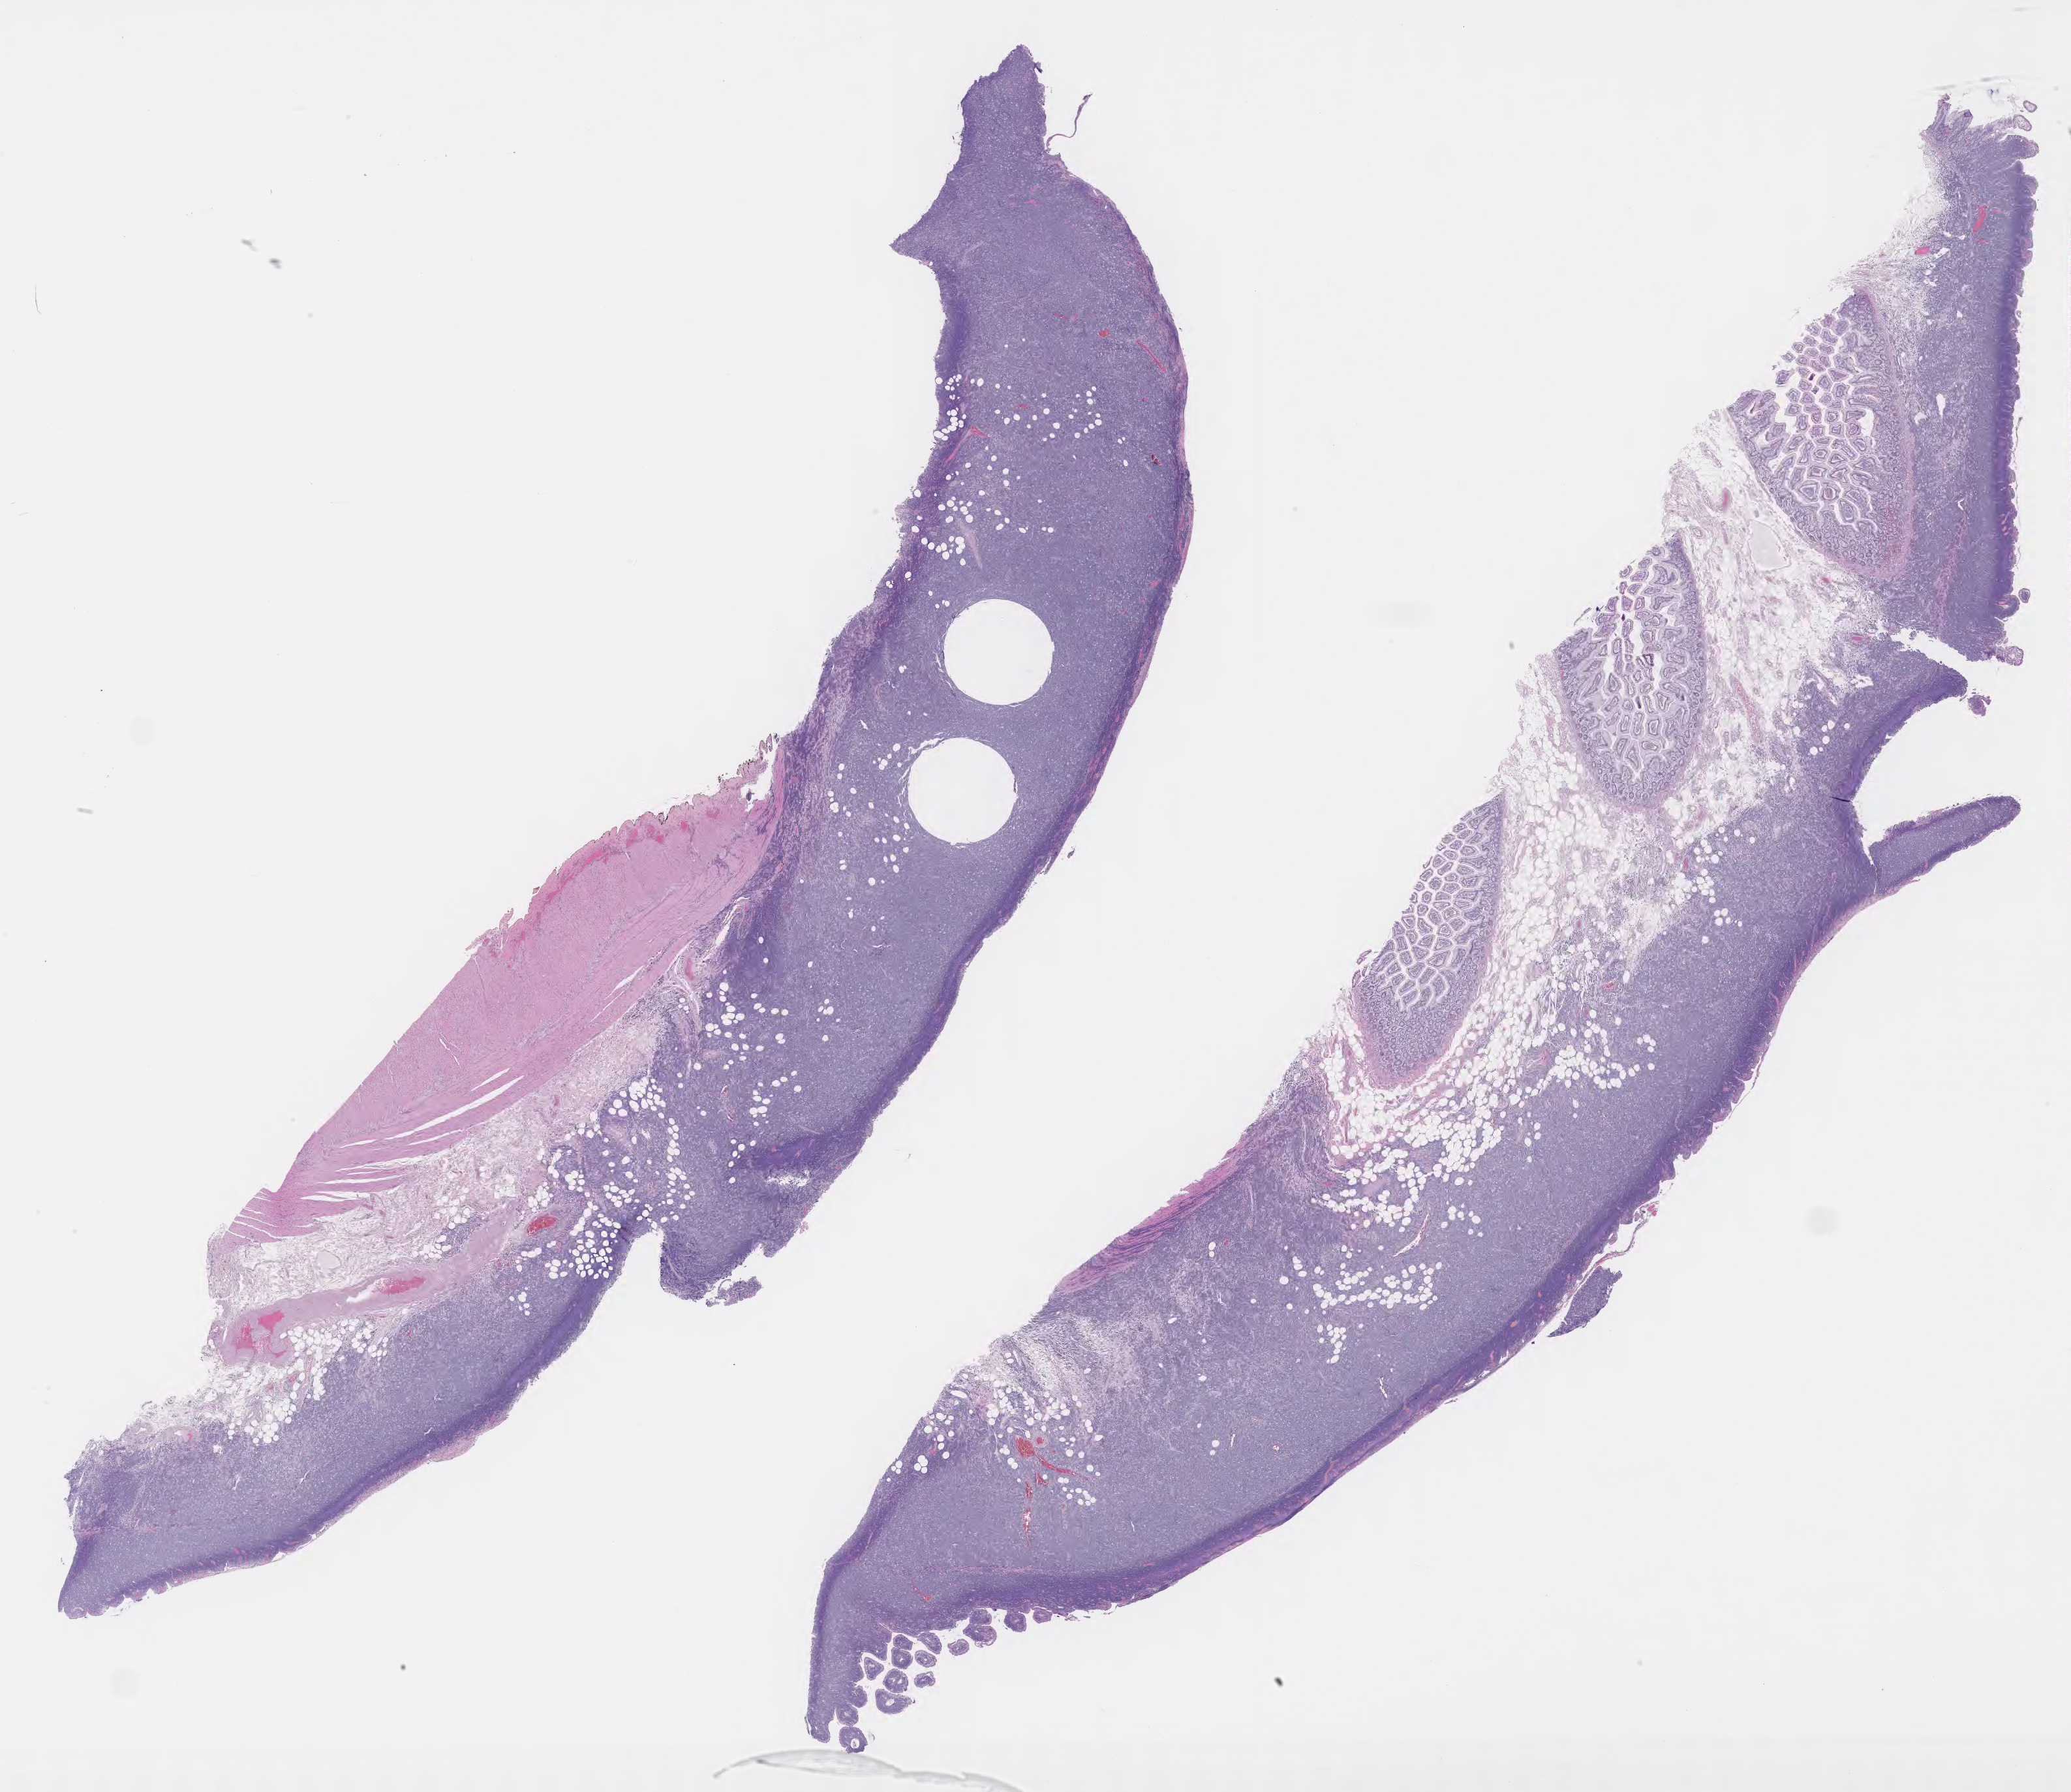
Whole-slide image, haematoxylin and eosin stain — a low-resolution overview of the entire scanned area, about 25.7 x 22.2 mm; tumor tissue; anatomic site: small intestine. Patient: male, aged 45.
• diagnosis: Burkitt lymphoma, NOS